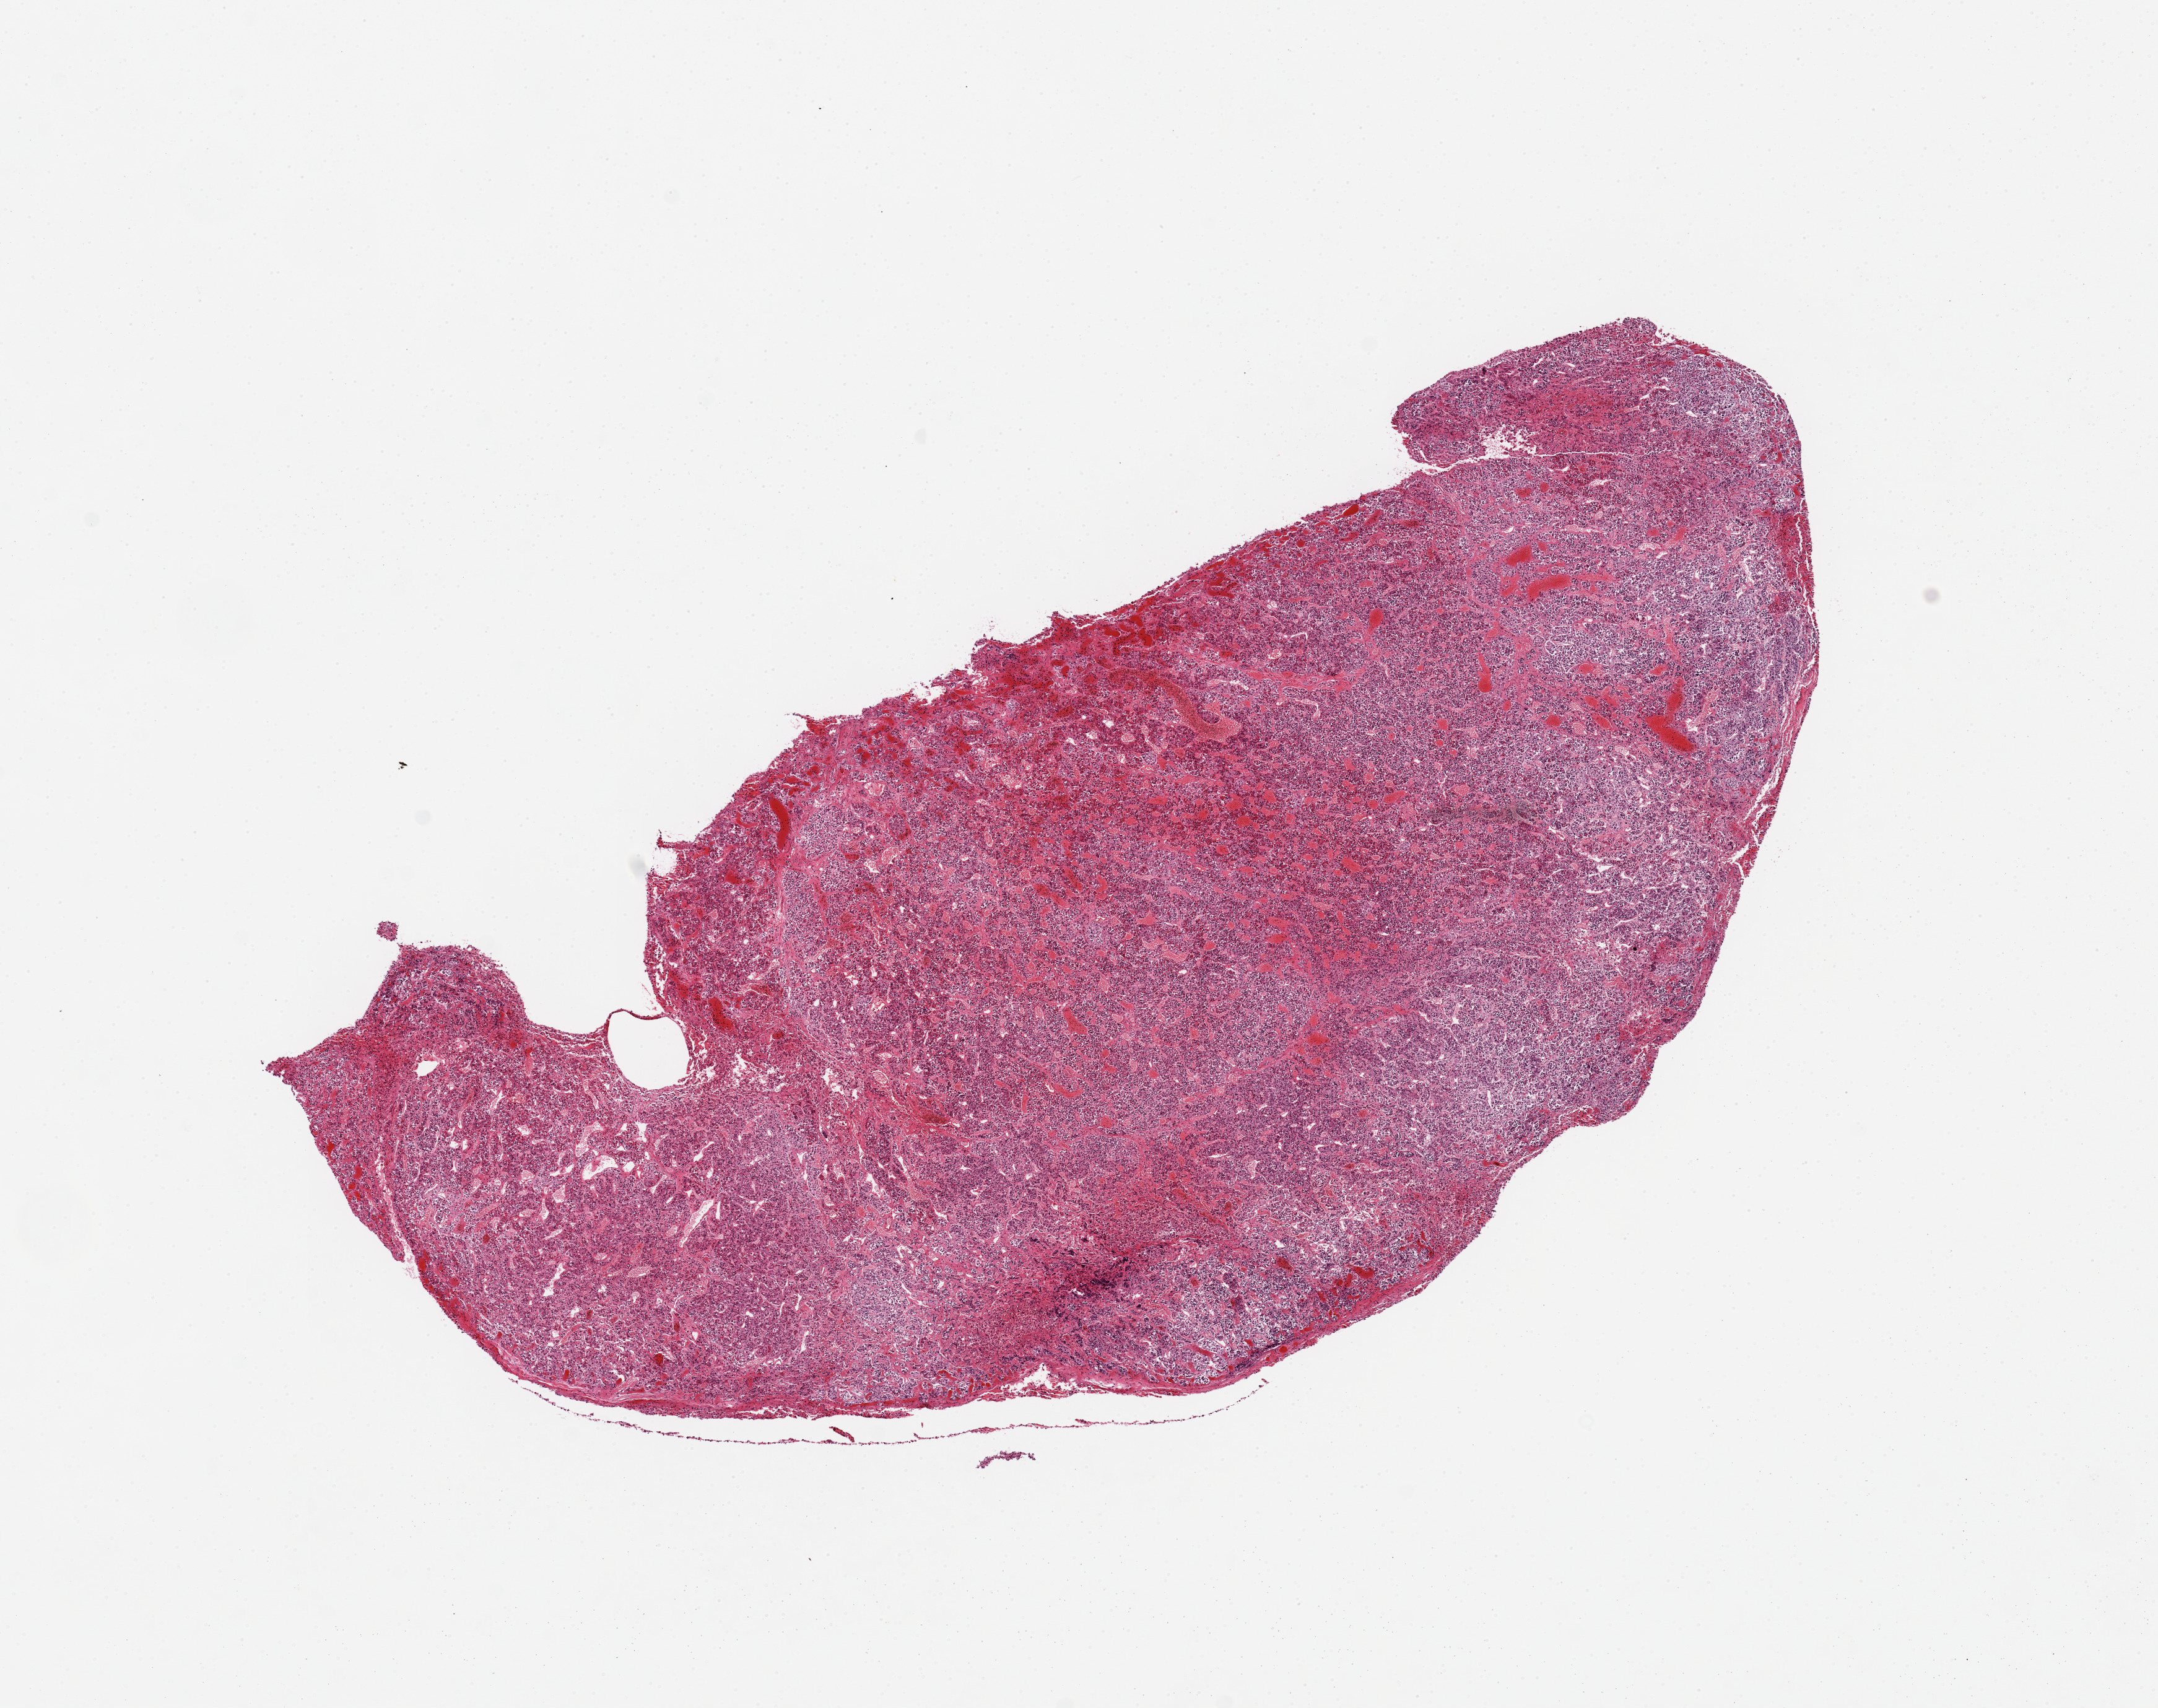
Hematoxylin and eosin (H&E) whole-slide image, whole scanned area (about 13.8 x 10.9 mm, from a 20x scan) shown as a low-resolution overview, PAXgene-fixed, paraffin-embedded tissue, target tissue: pituitary, tissue donor sample. Male donor.
Pathologist's review note for this sample: 1 piece; anterior.